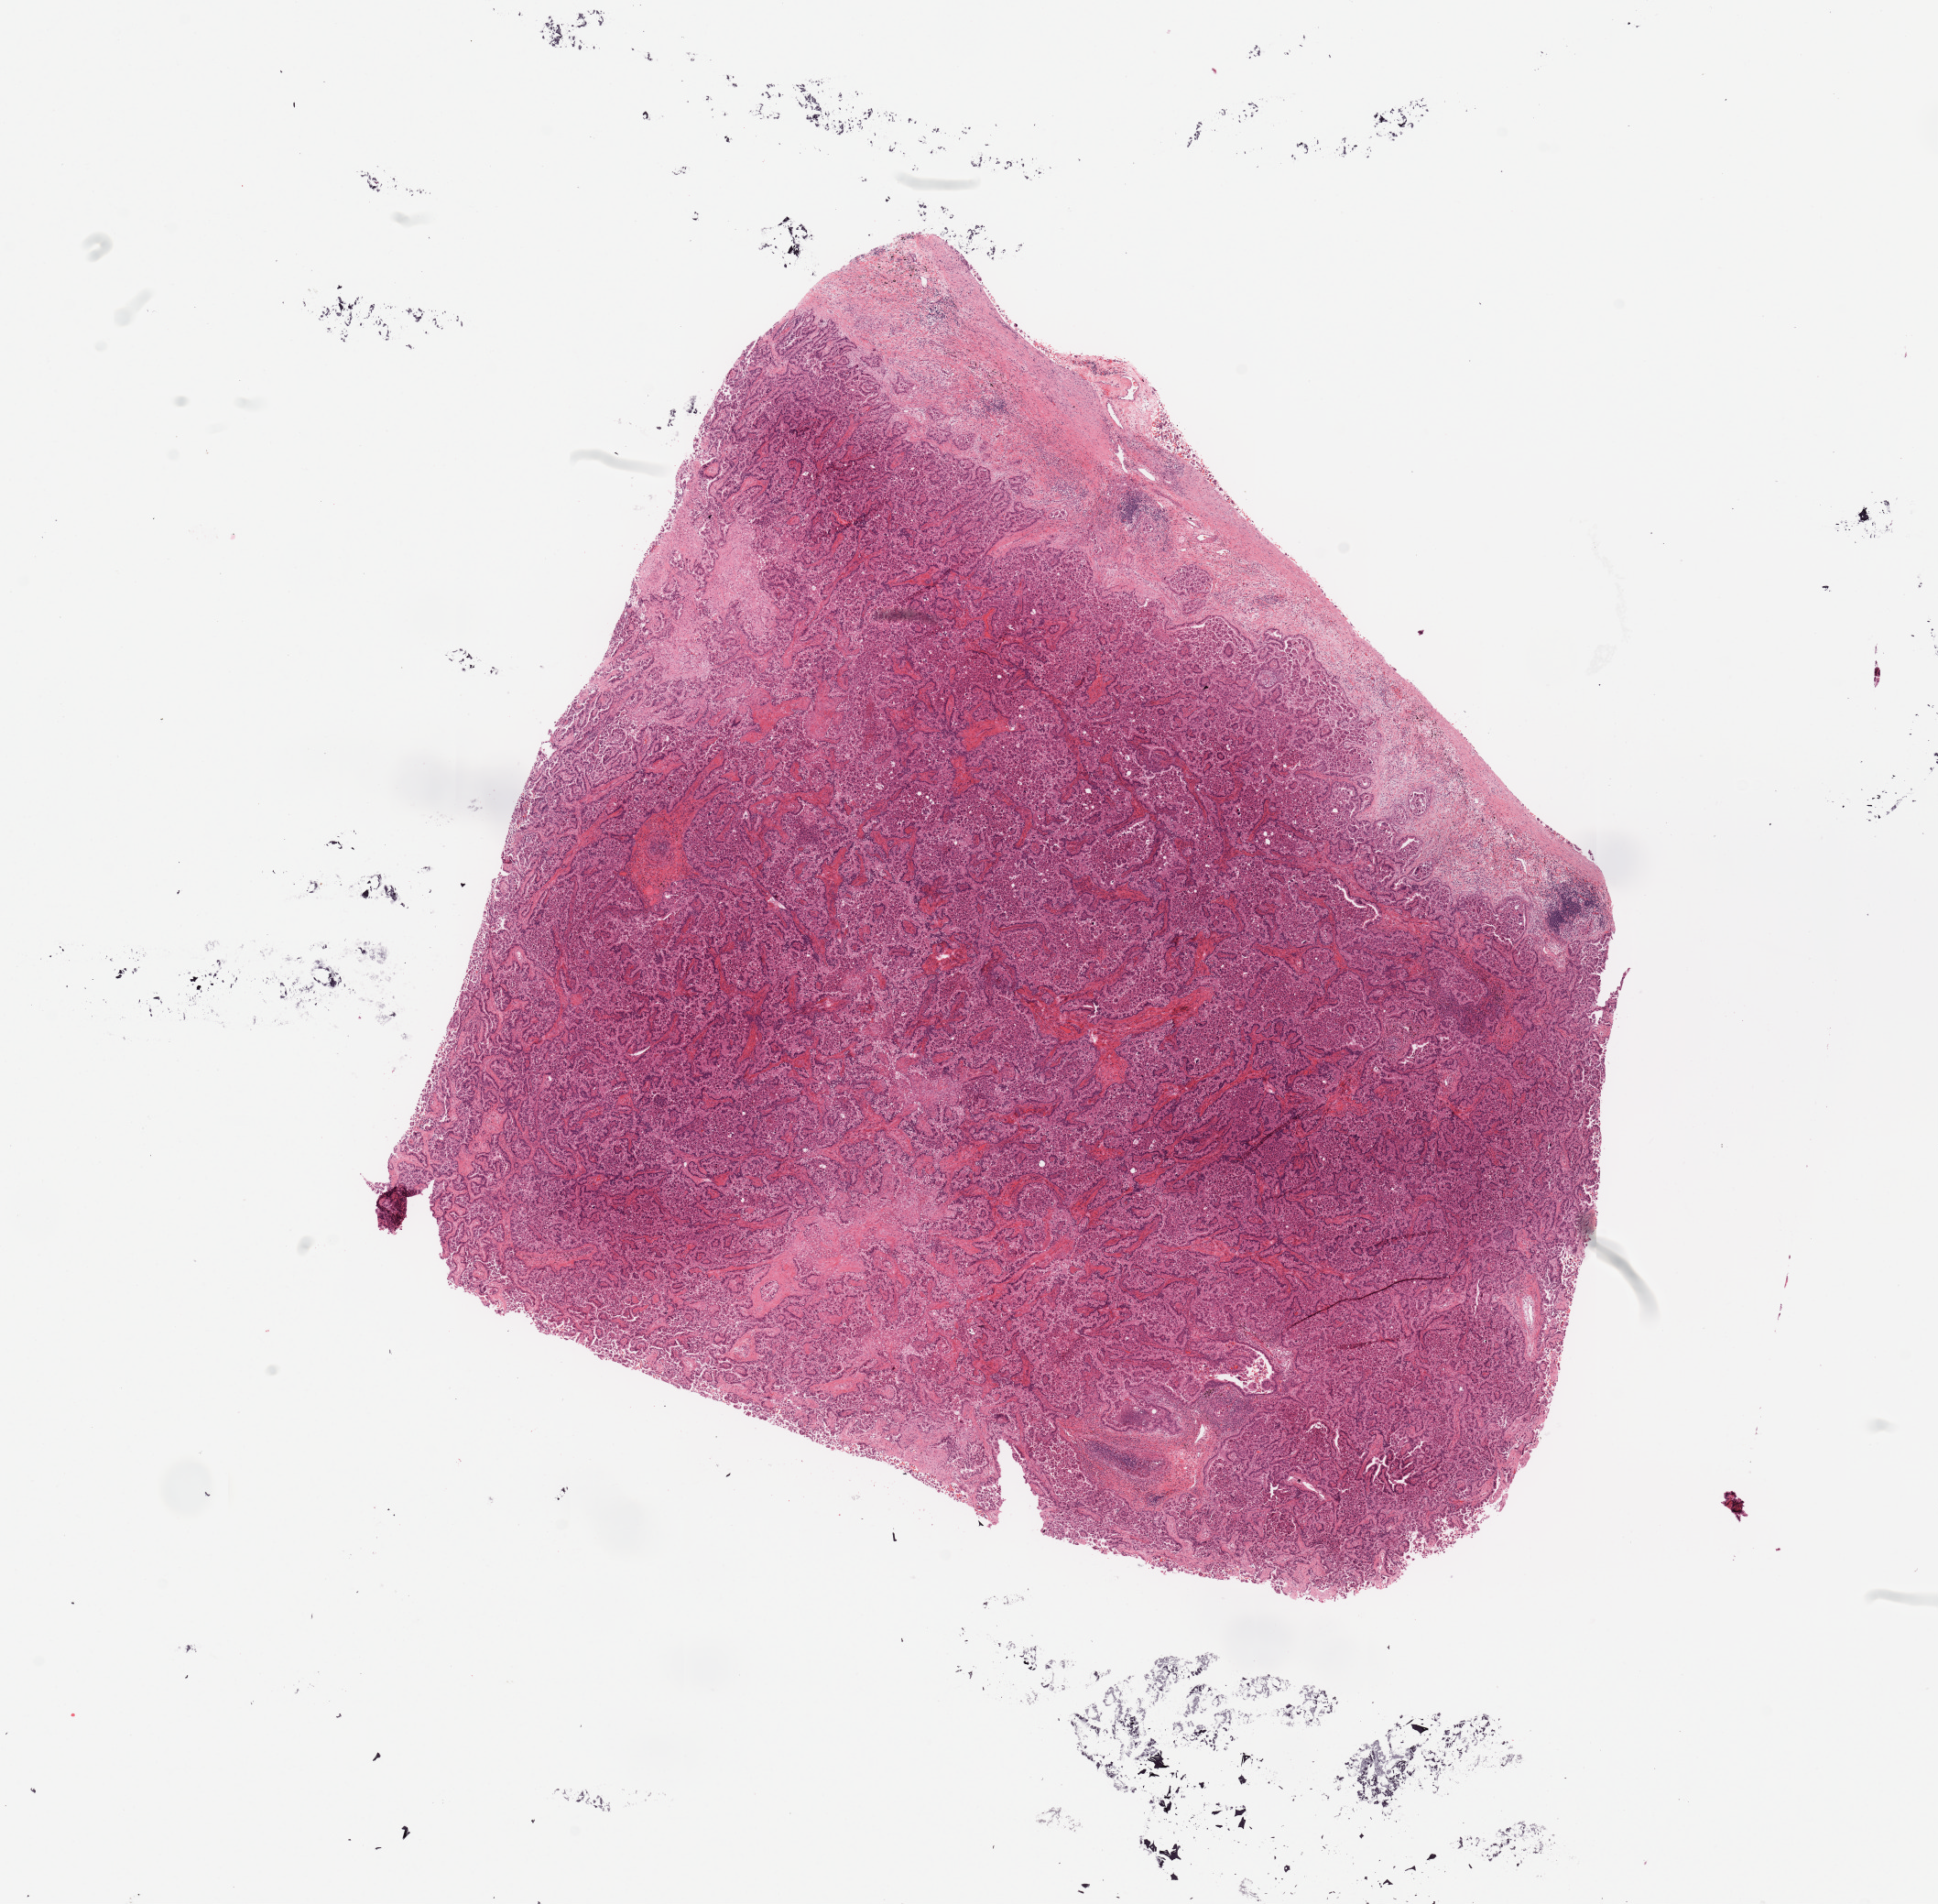
Digitized Hematoxylin and eosin (H&E) stained tissue section (whole slide), shown as a low-resolution overview of the whole scanned area (about 16.7 x 16.4 mm, acquisition: 20x scan). Tumour tissue sample, sampled site: lung. 45-year-old male patient. Histologic grade: G3 (poorly differentiated). Slide review estimates, as recorded: tumour nuclei 80%, necrosis 5%.
AJCC pathologic stage: IB. Histologic diagnosis: Adenocarcinoma, NOS. Primary tumour site (as recorded): left upper lobe.